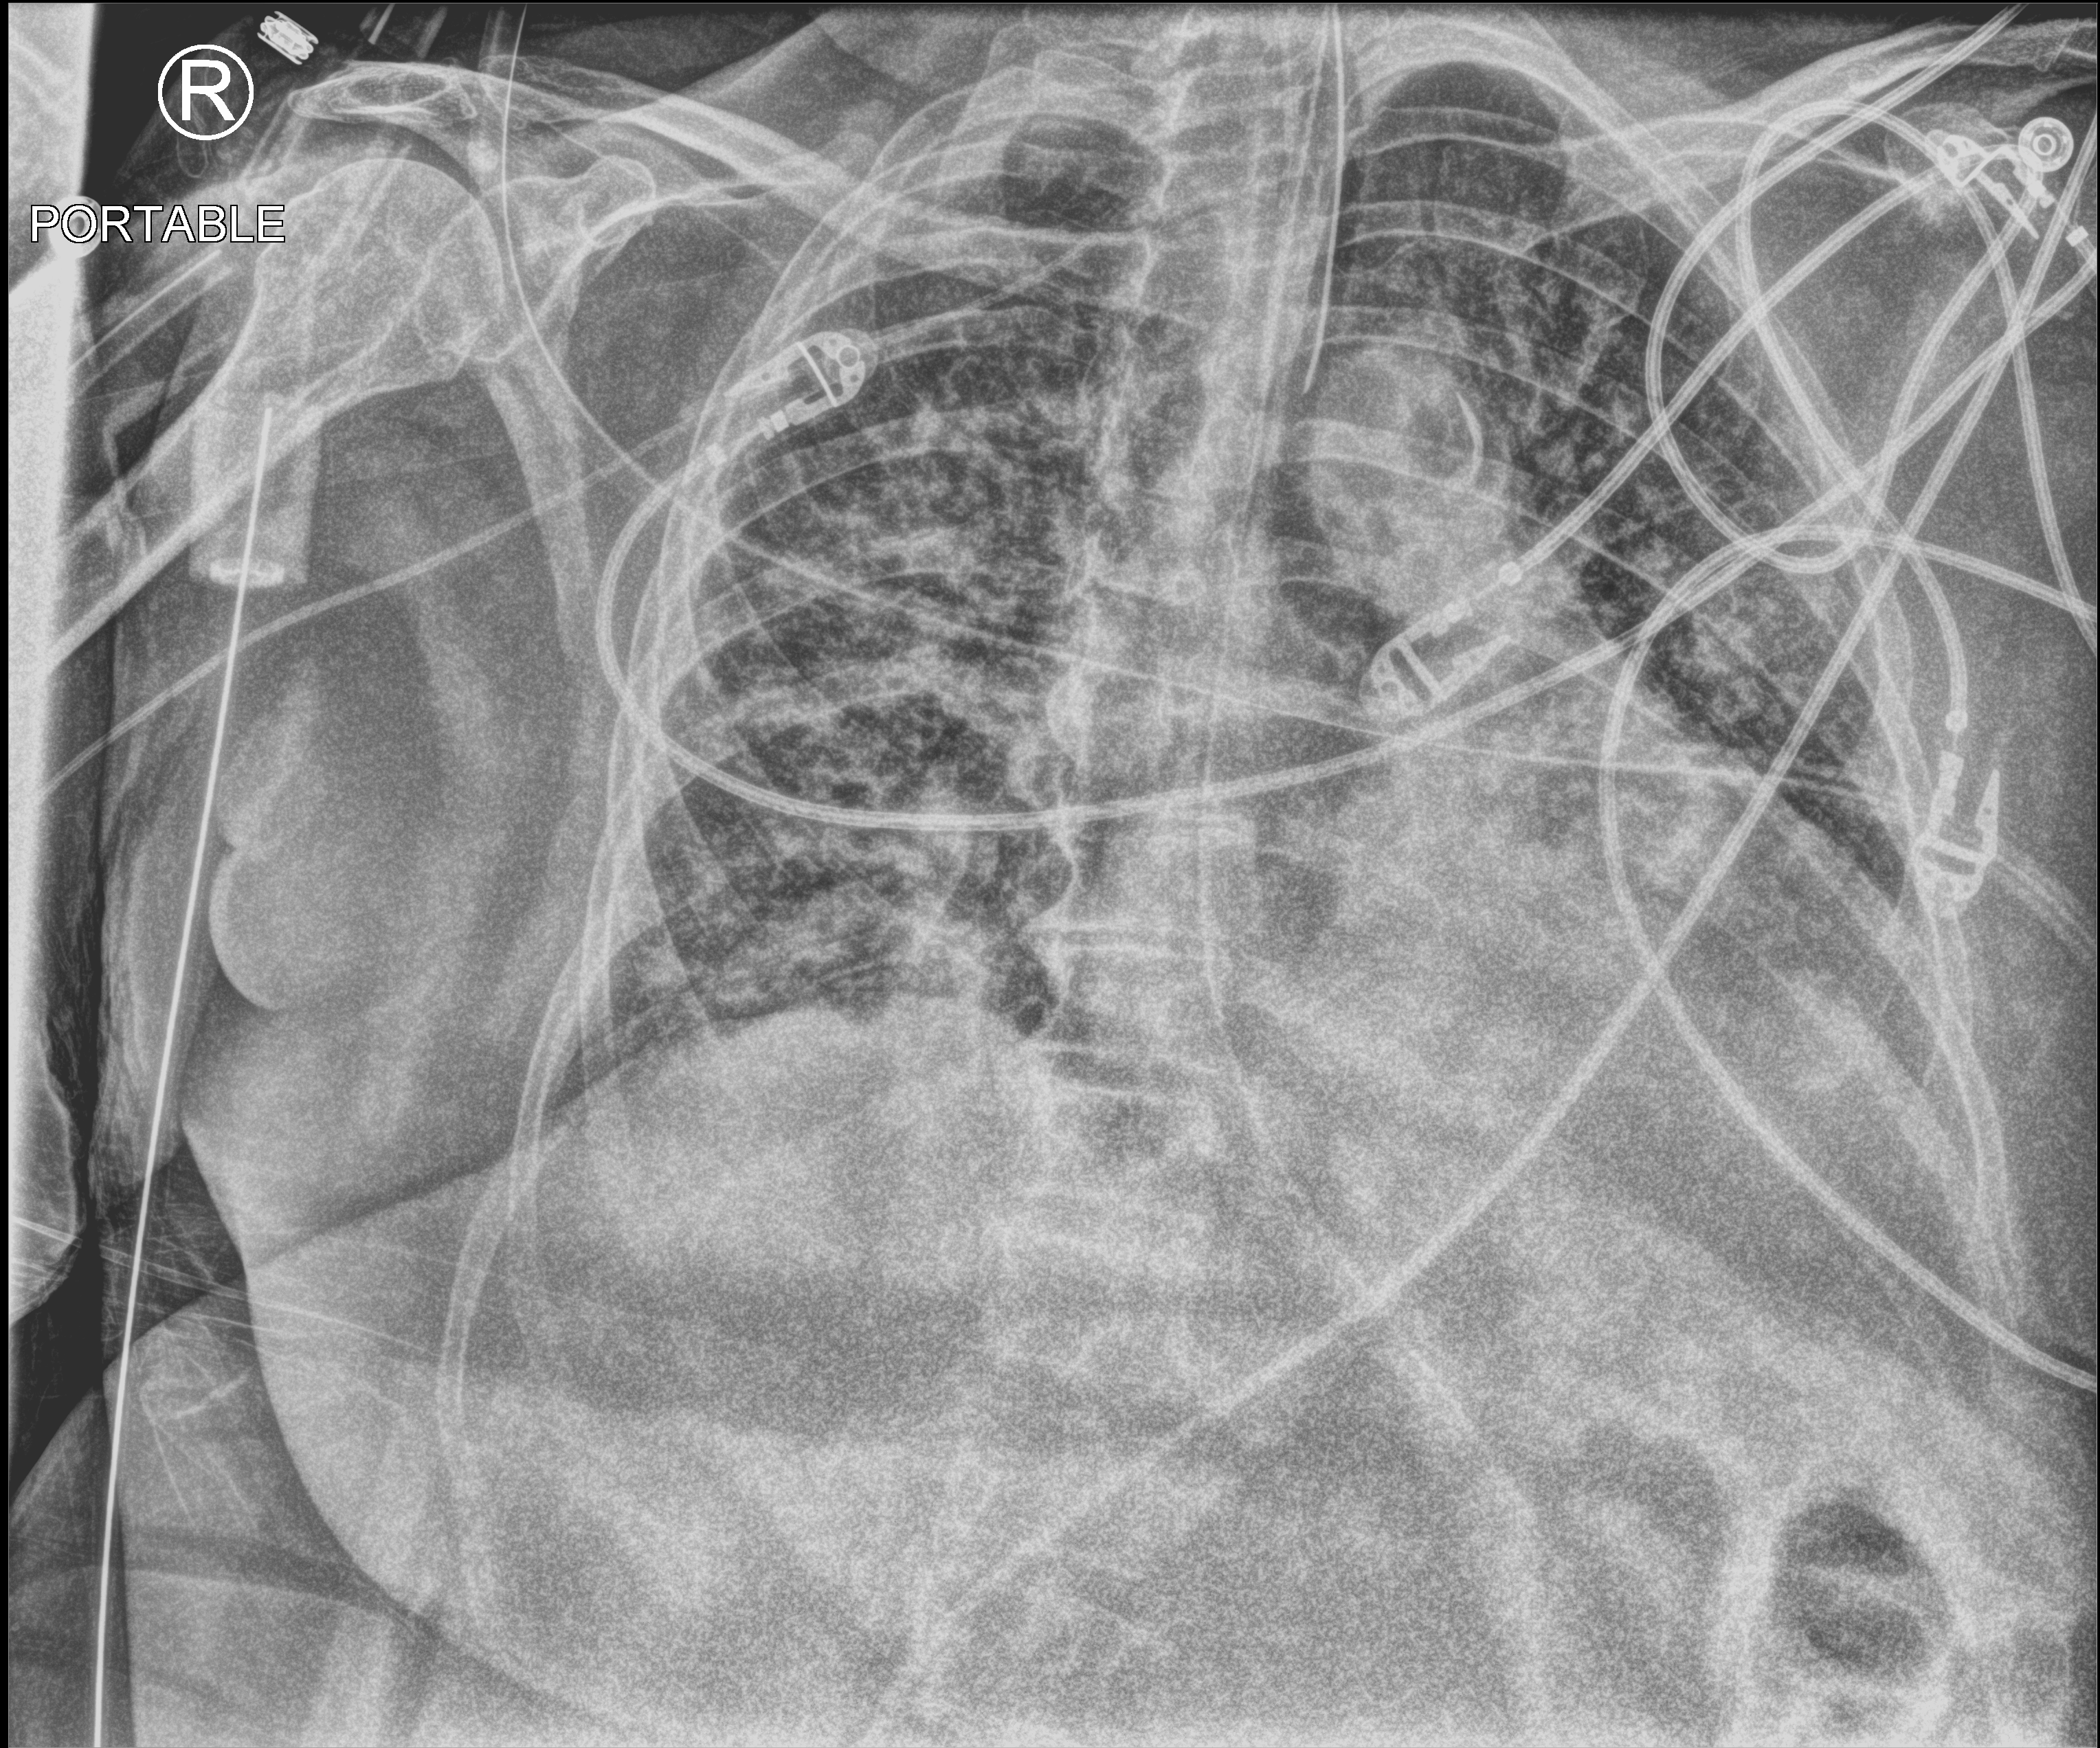
Portable chest radiograph; anteroposterior (AP) projection. Female patient hospitalised with COVID-19, age 75–90 years.
Hospital-stay facts (about this admission, not read from this image; timing relative to this image not recorded): length of hospital stay: 31 days; mechanically ventilated during this hospital stay: yes.